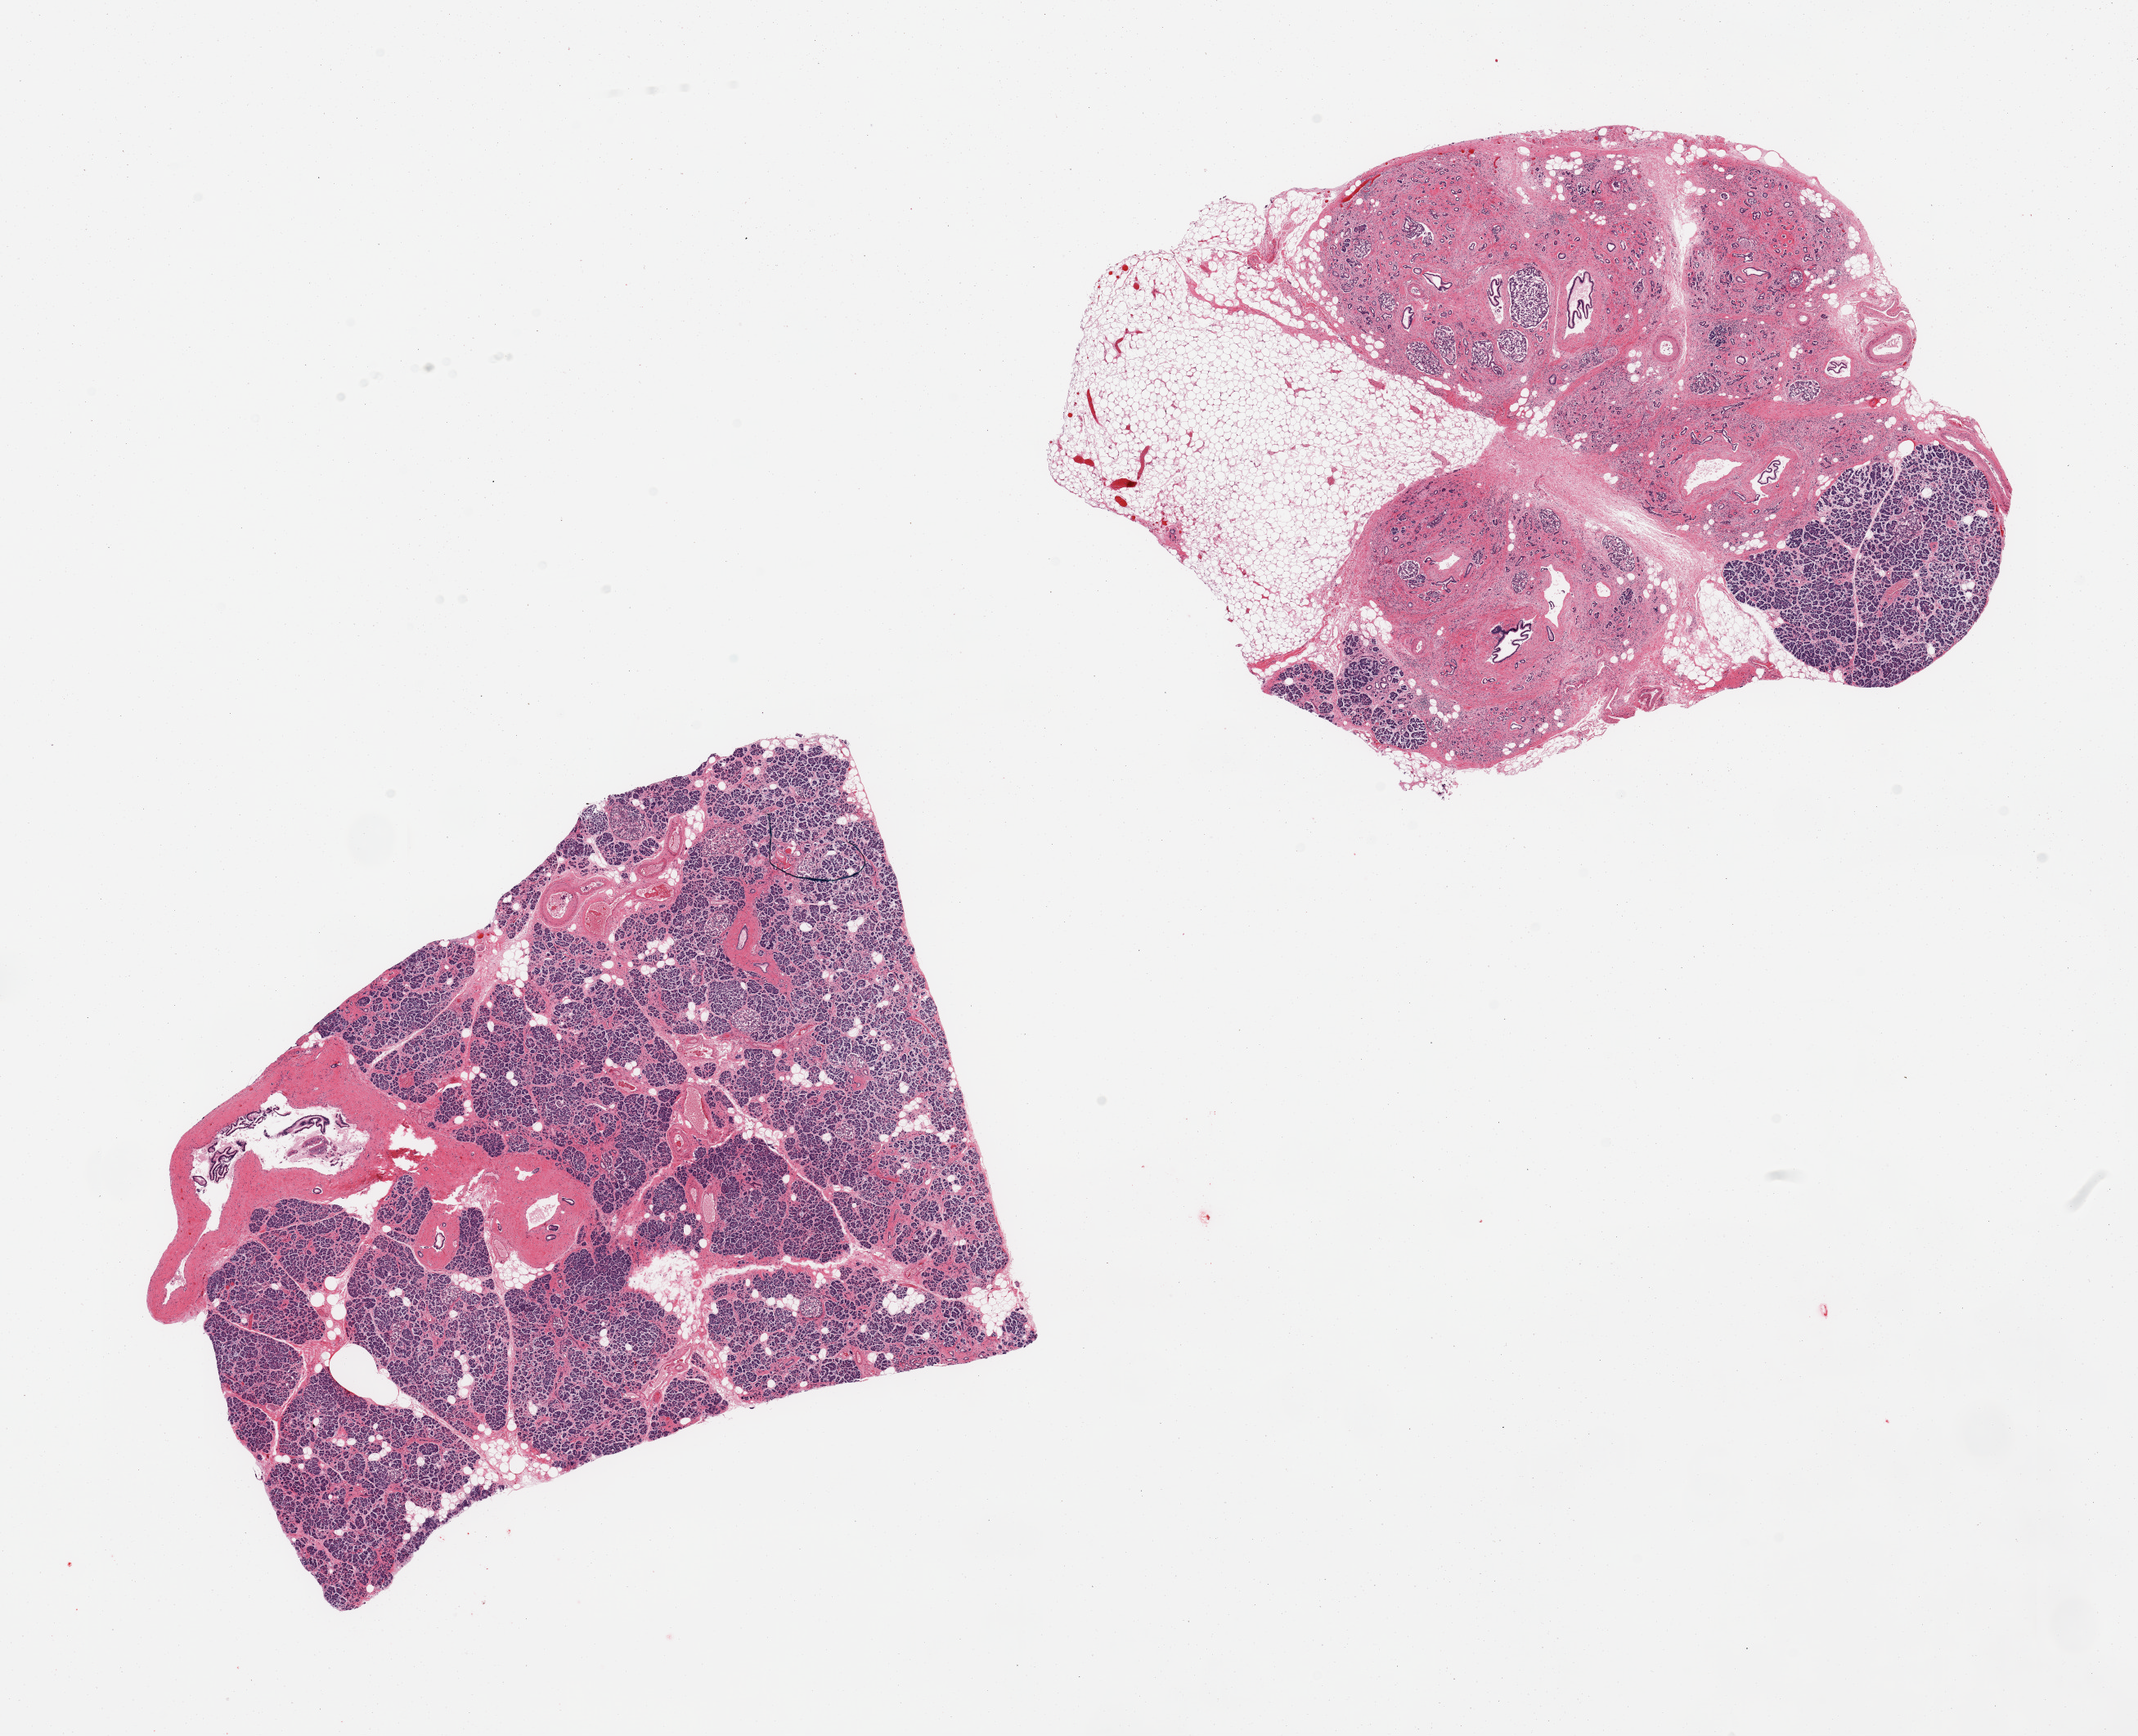
Whole-slide image, H&E stain — whole scanned area (about 20.7 x 16.8 mm, acquisition: 20x scan) shown as a low-resolution overview; PAXgene-fixed paraffin-embedded (PFPE) section; section of pancreas (target tissue); tissue donor sample. Donor sex: male.
• review note (as recorded): 2 pieces, some areas approach autolysis score two; Area of fibrotic remote pancreatitis; Reasonably well-preserved Islets